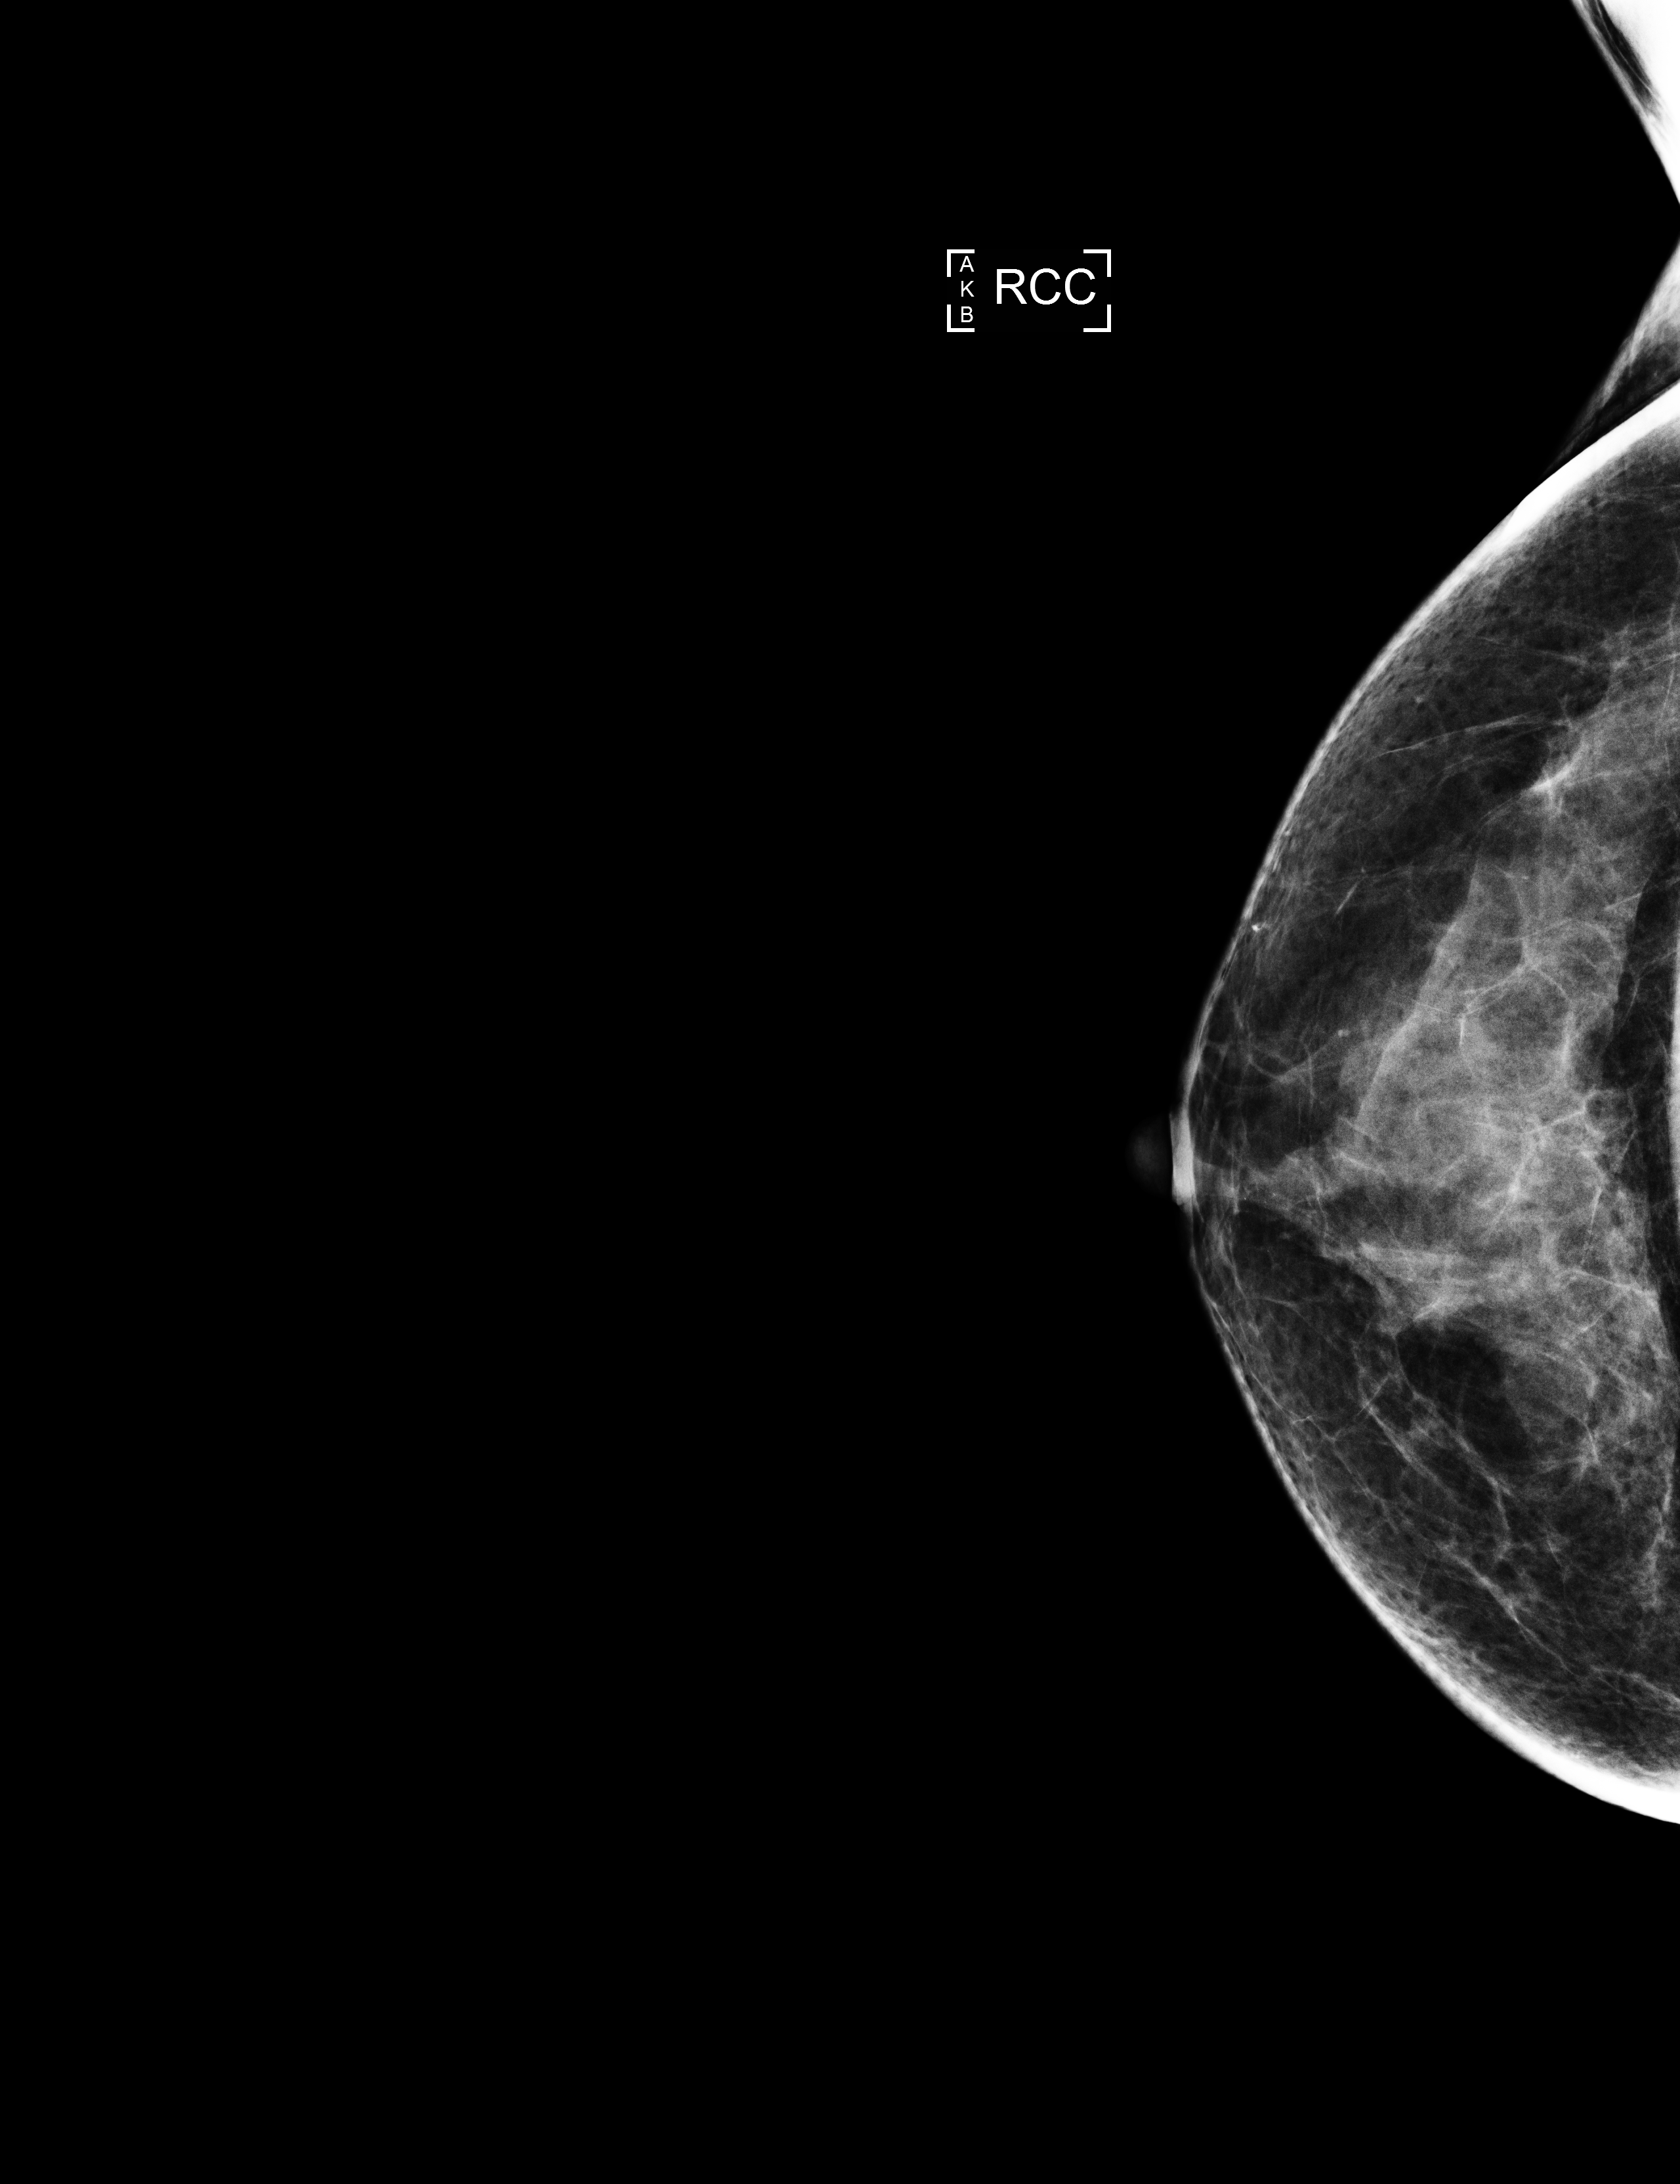
Full-field digital mammogram (FFDM), right breast, craniocaudal (CC) view, screening examination, compressed breast thickness 45 mm. Patient: female, 57 years.
Breast density at the screening exam (both breasts): heterogeneously dense (BI-RADS density category c). Final BI-RADS category for the screening round (tomosynthesis exam, both breasts): category 1. Recall: no recall after this screen.